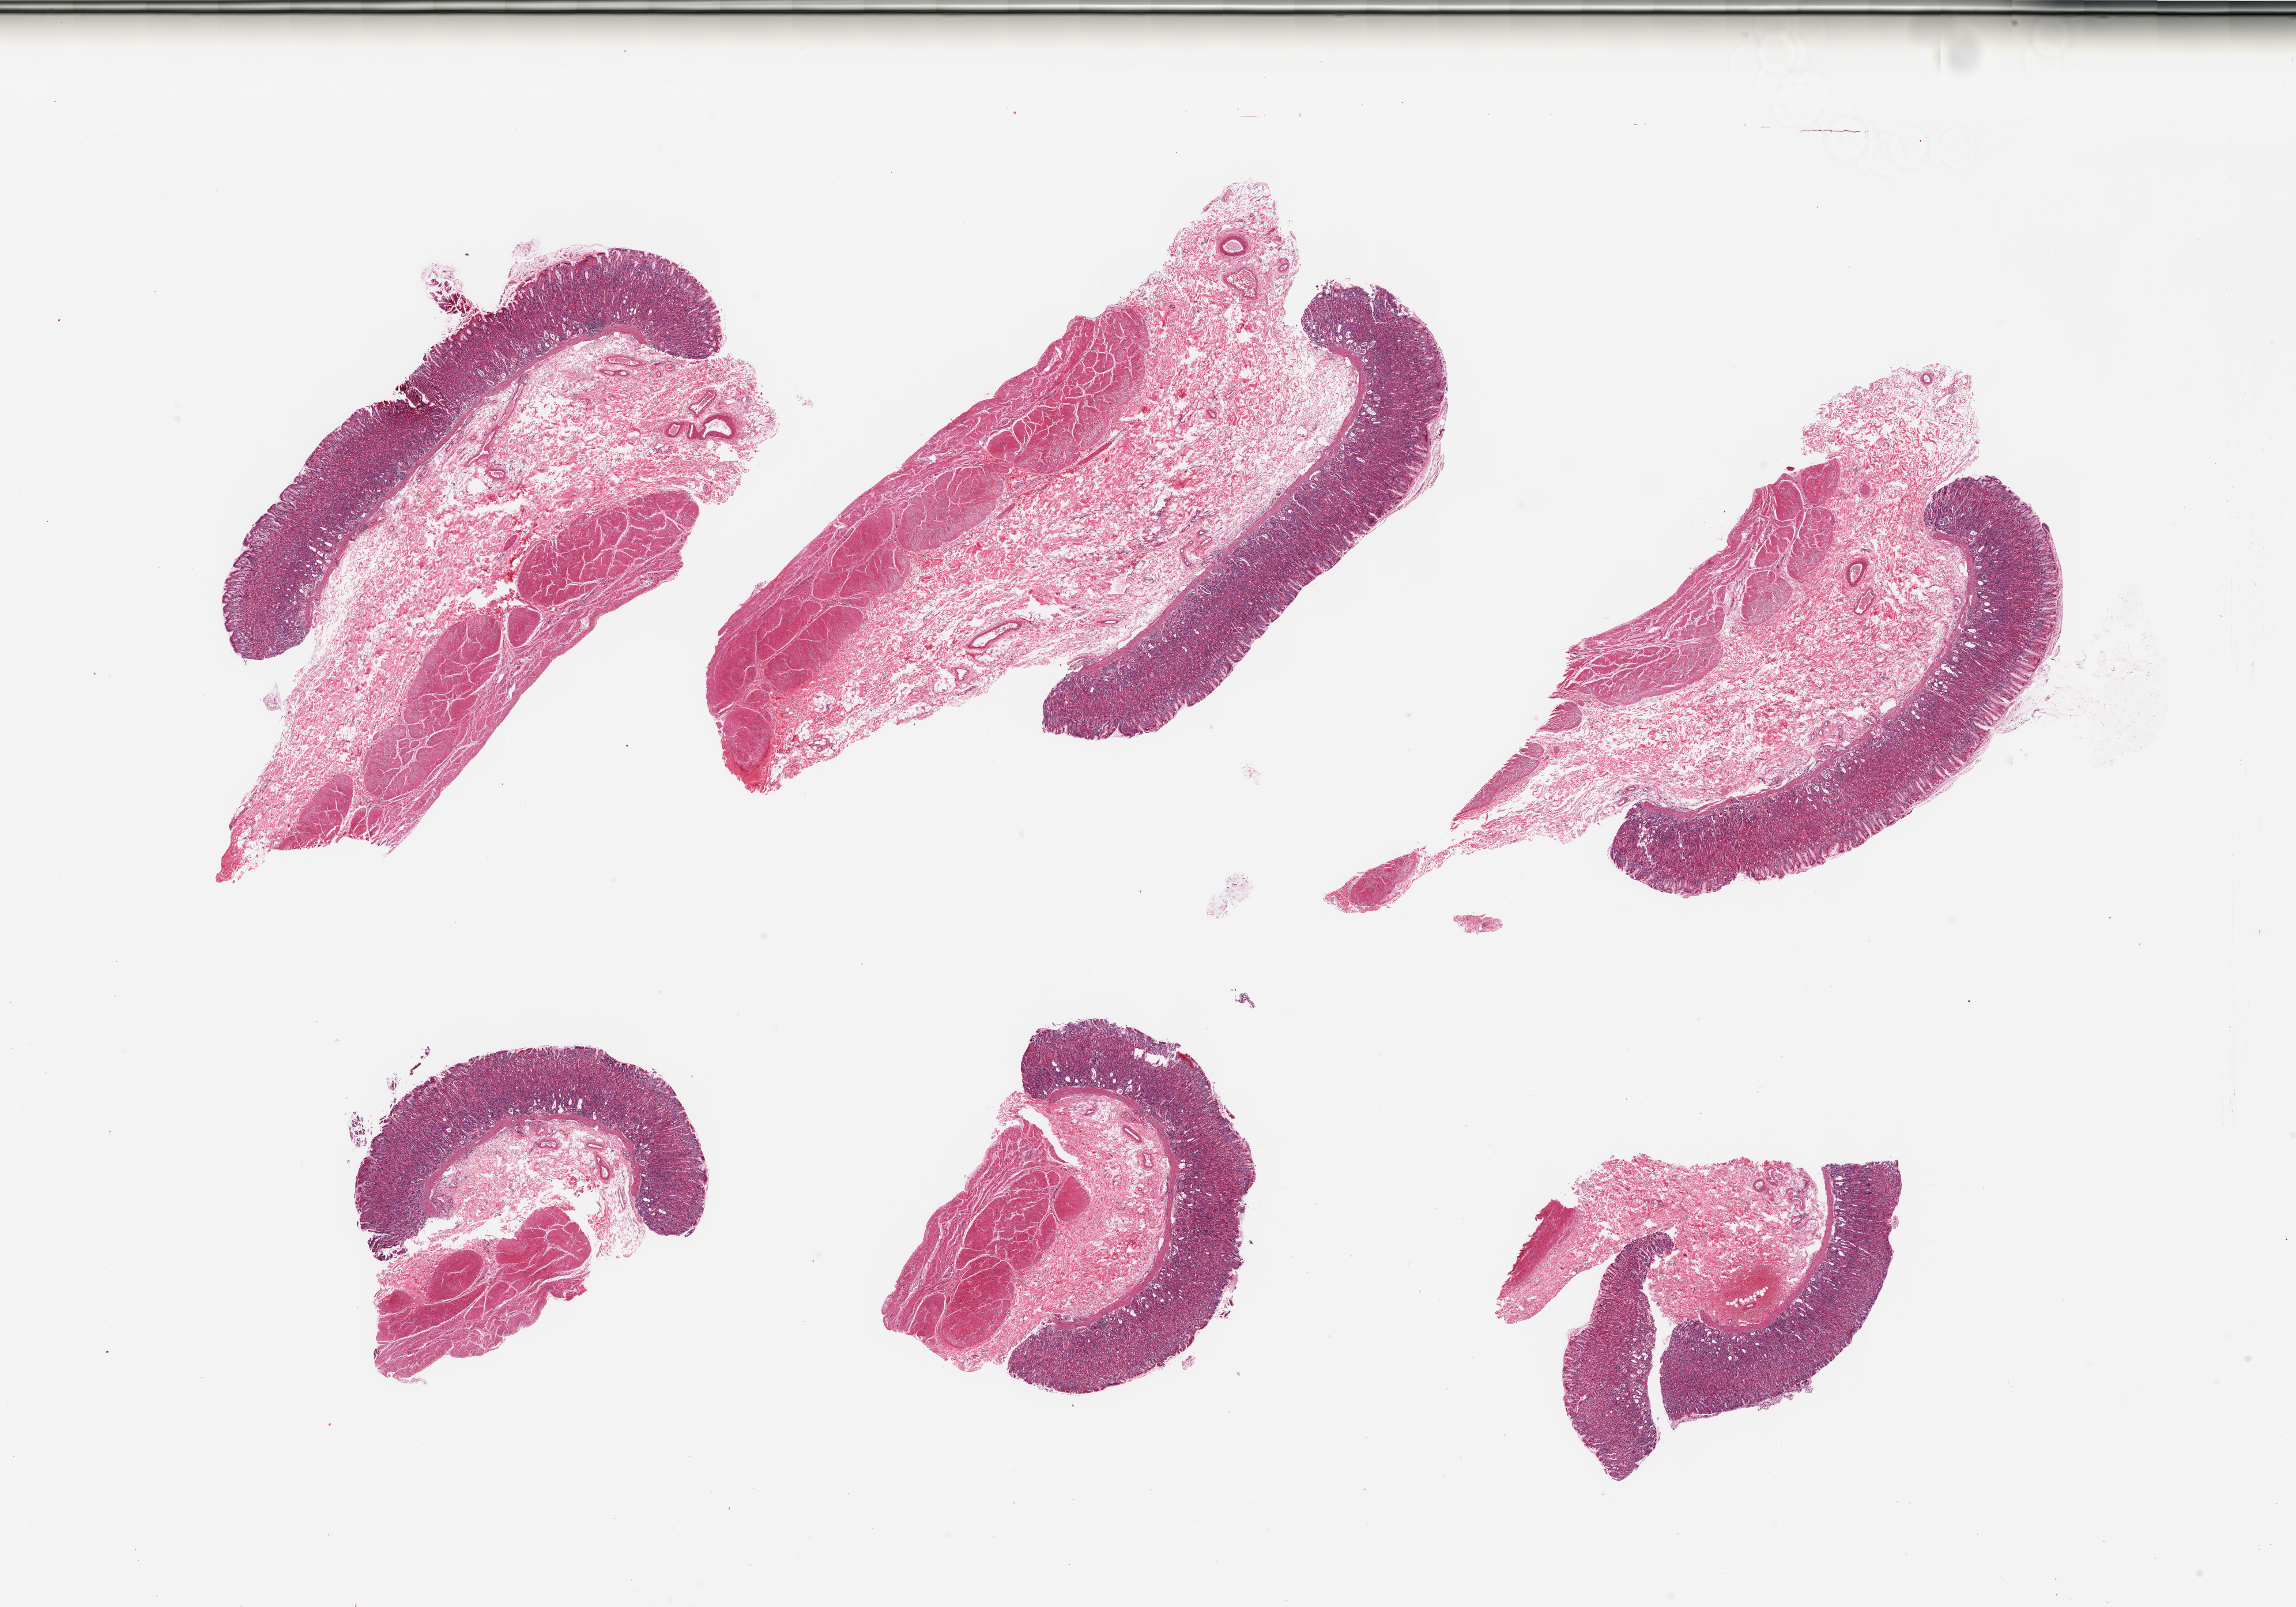
H&E whole-slide image, a low-resolution overview of the entire scanned area, about 31.5 x 22.0 mm. Female donor.
Specimen: PAXgene-fixed, paraffin-embedded tissue; sampled site (target tissue): stomach; donor tissue sample.